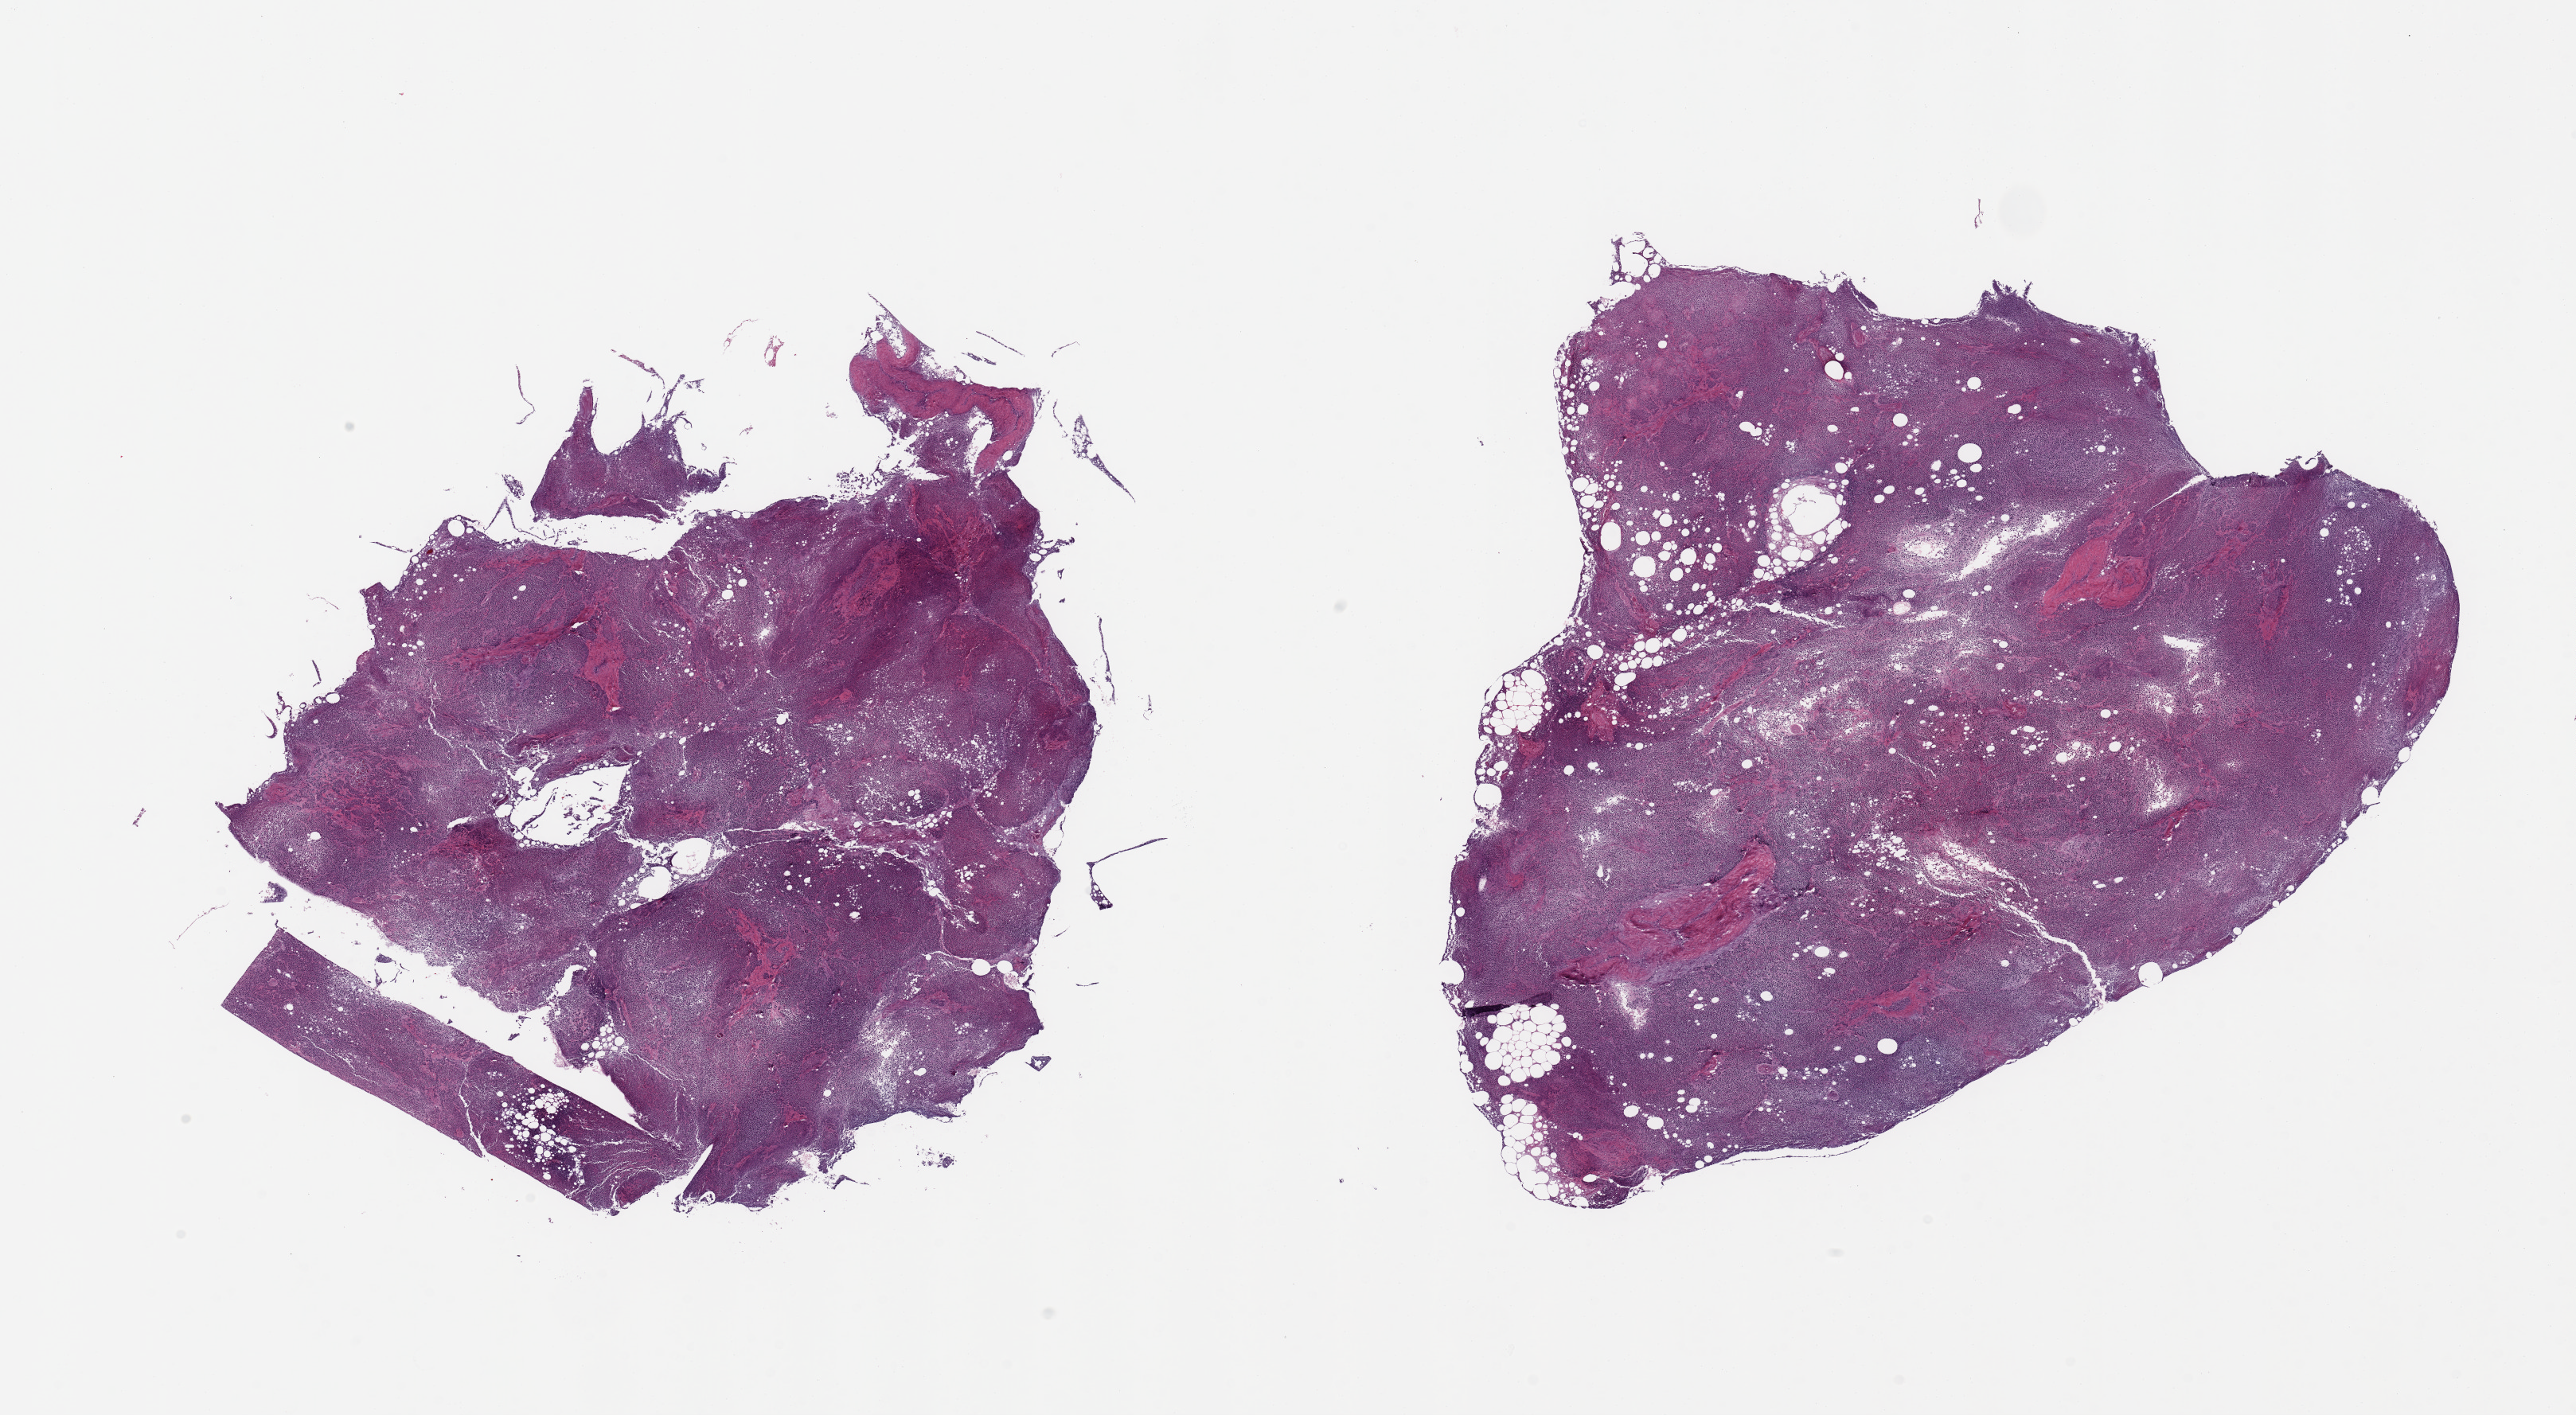
Whole-slide image, hematoxylin and eosin (H&E) stain, a low-resolution overview of the entire scanned area, about 25.6 x 14.1 mm (slide scanned at 20x), PAXgene-fixed paraffin-embedded (PFPE) section, sampled site (target tissue): pancreas, tissue donor sample. Donor sex: male.
Reviewer comment on this tissue sample: 2 pieces; autolyzed.